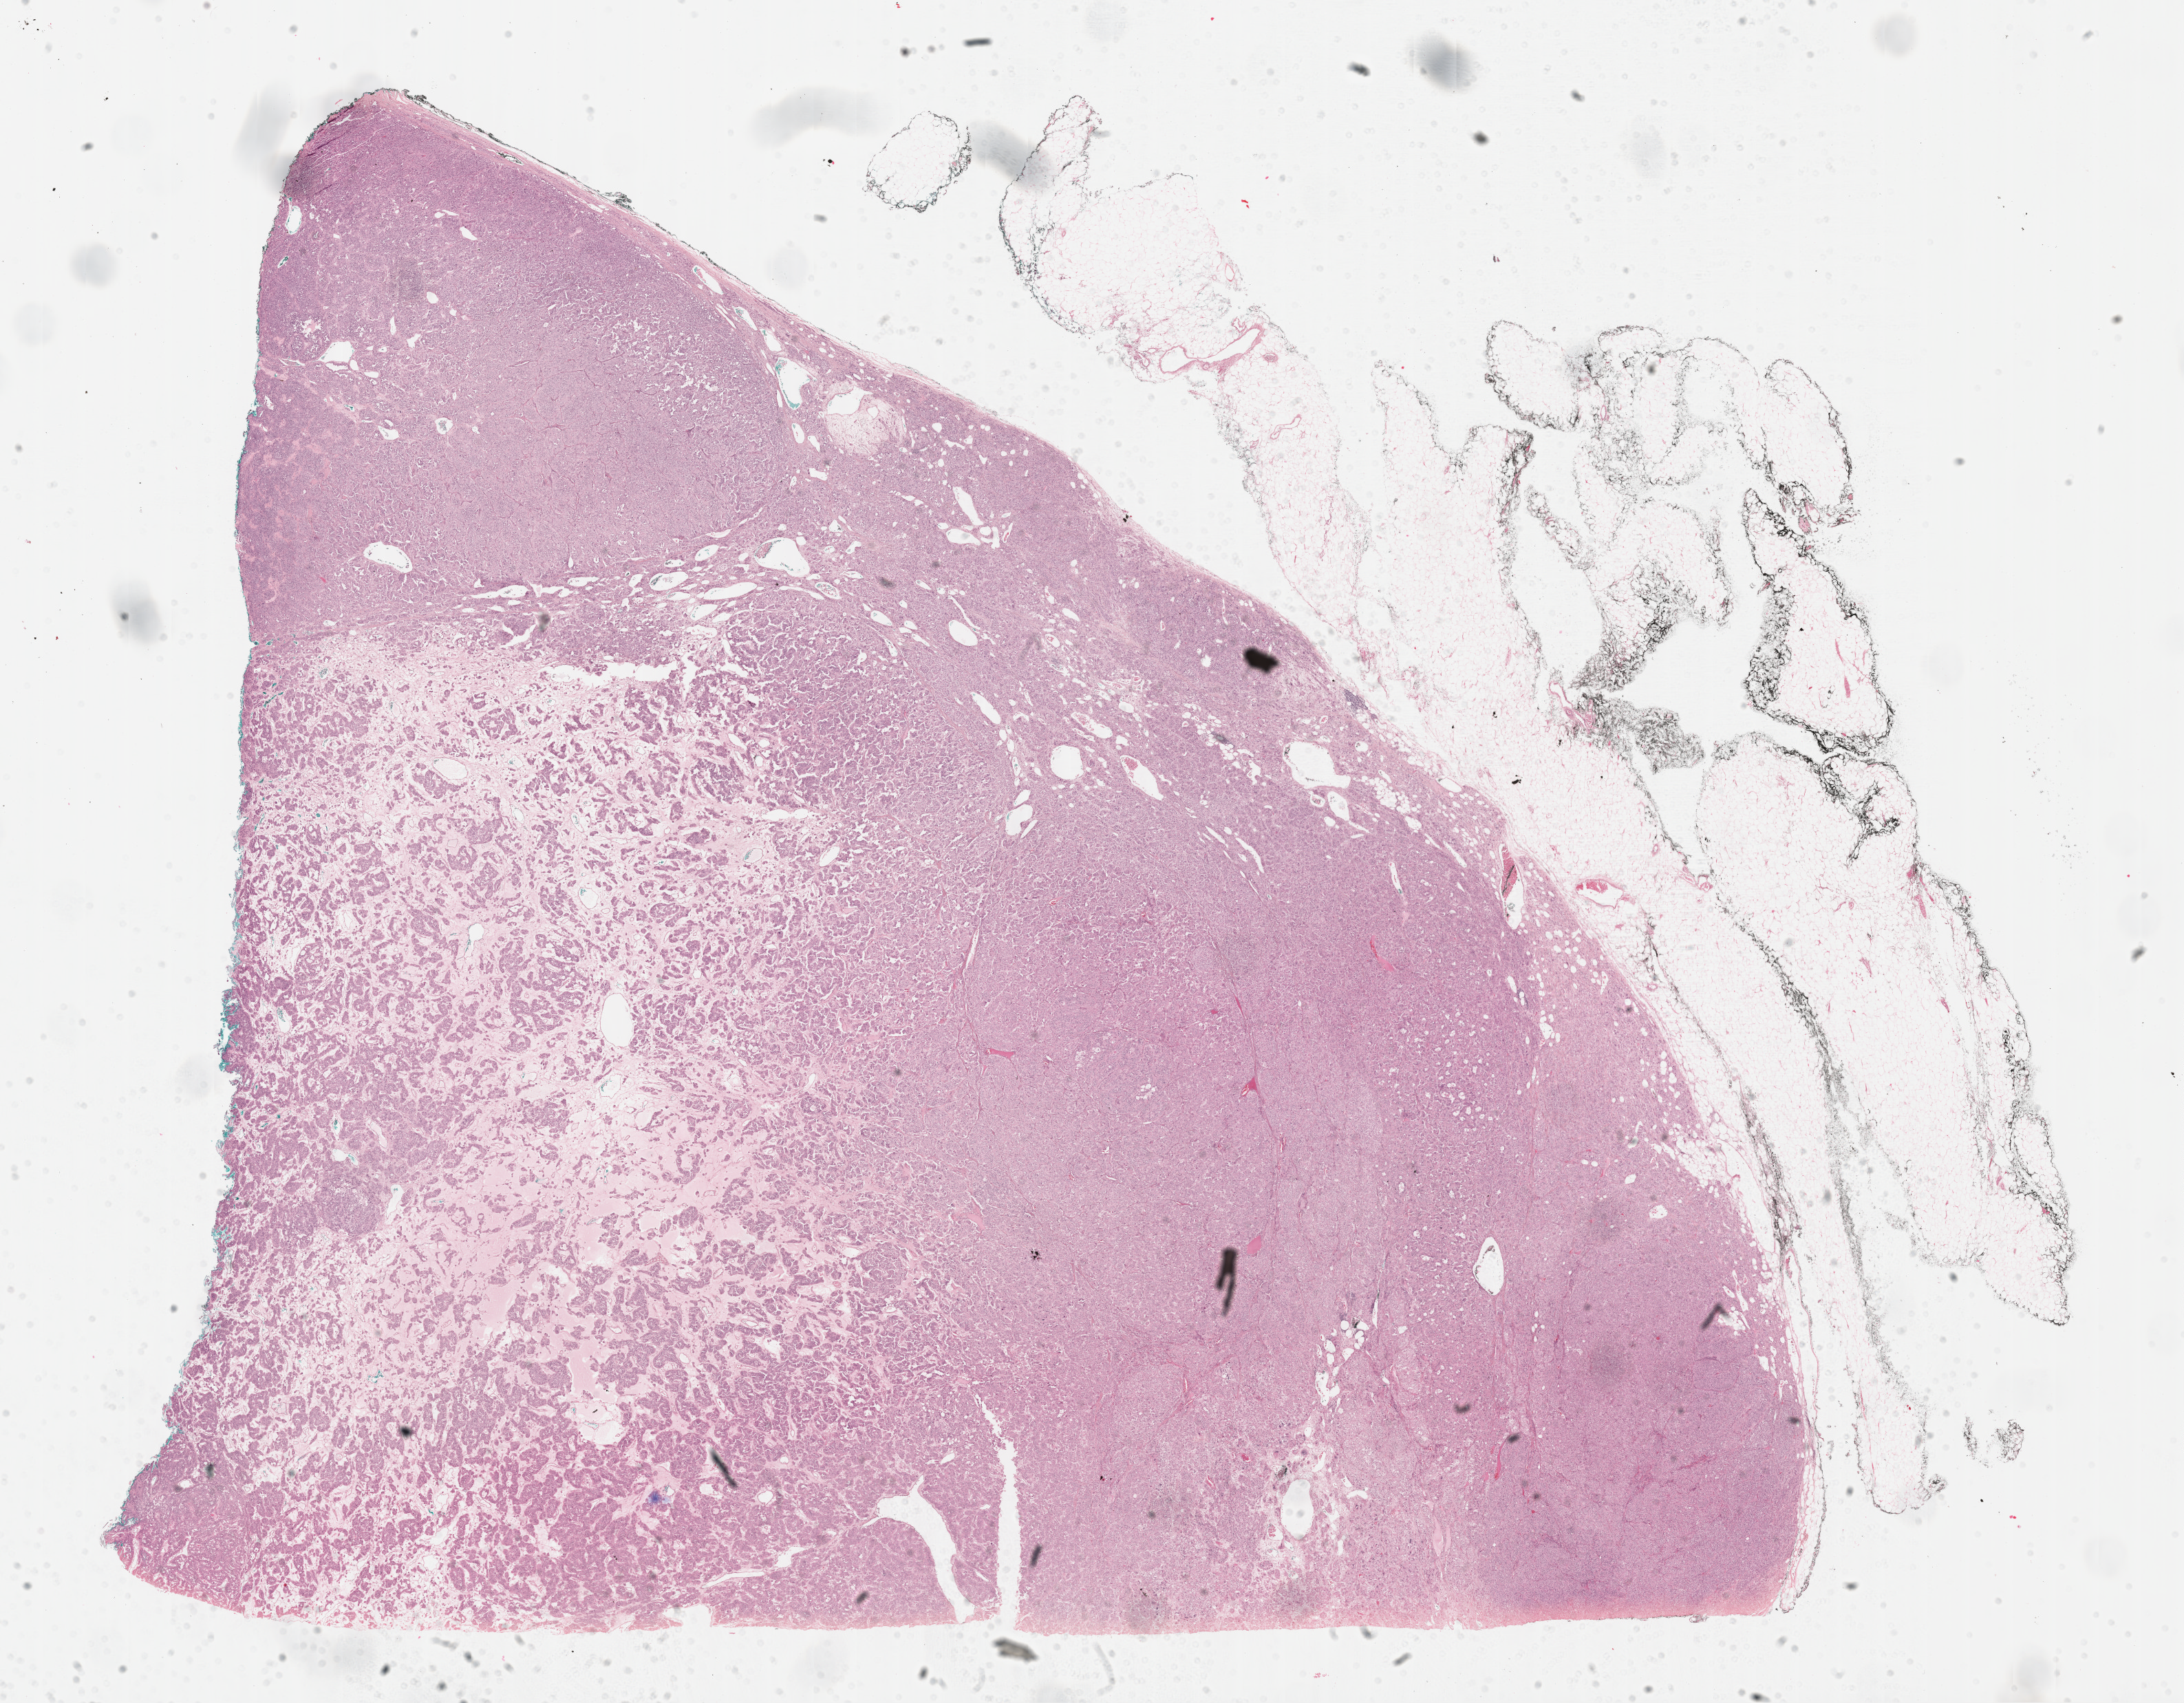
Digitized H&E-stained tissue section (whole slide) — shown as a low-resolution overview of the whole scanned area (about 25.7 x 20.0 mm, slide scanned at 40x); formalin-fixed paraffin-embedded (FFPE) diagnostic section; primary tumour sample from the adrenal cortex. Female, age 69 years at initial diagnosis.
Diagnosis: Adrenal cortical carcinoma (cortex of adrenal gland).